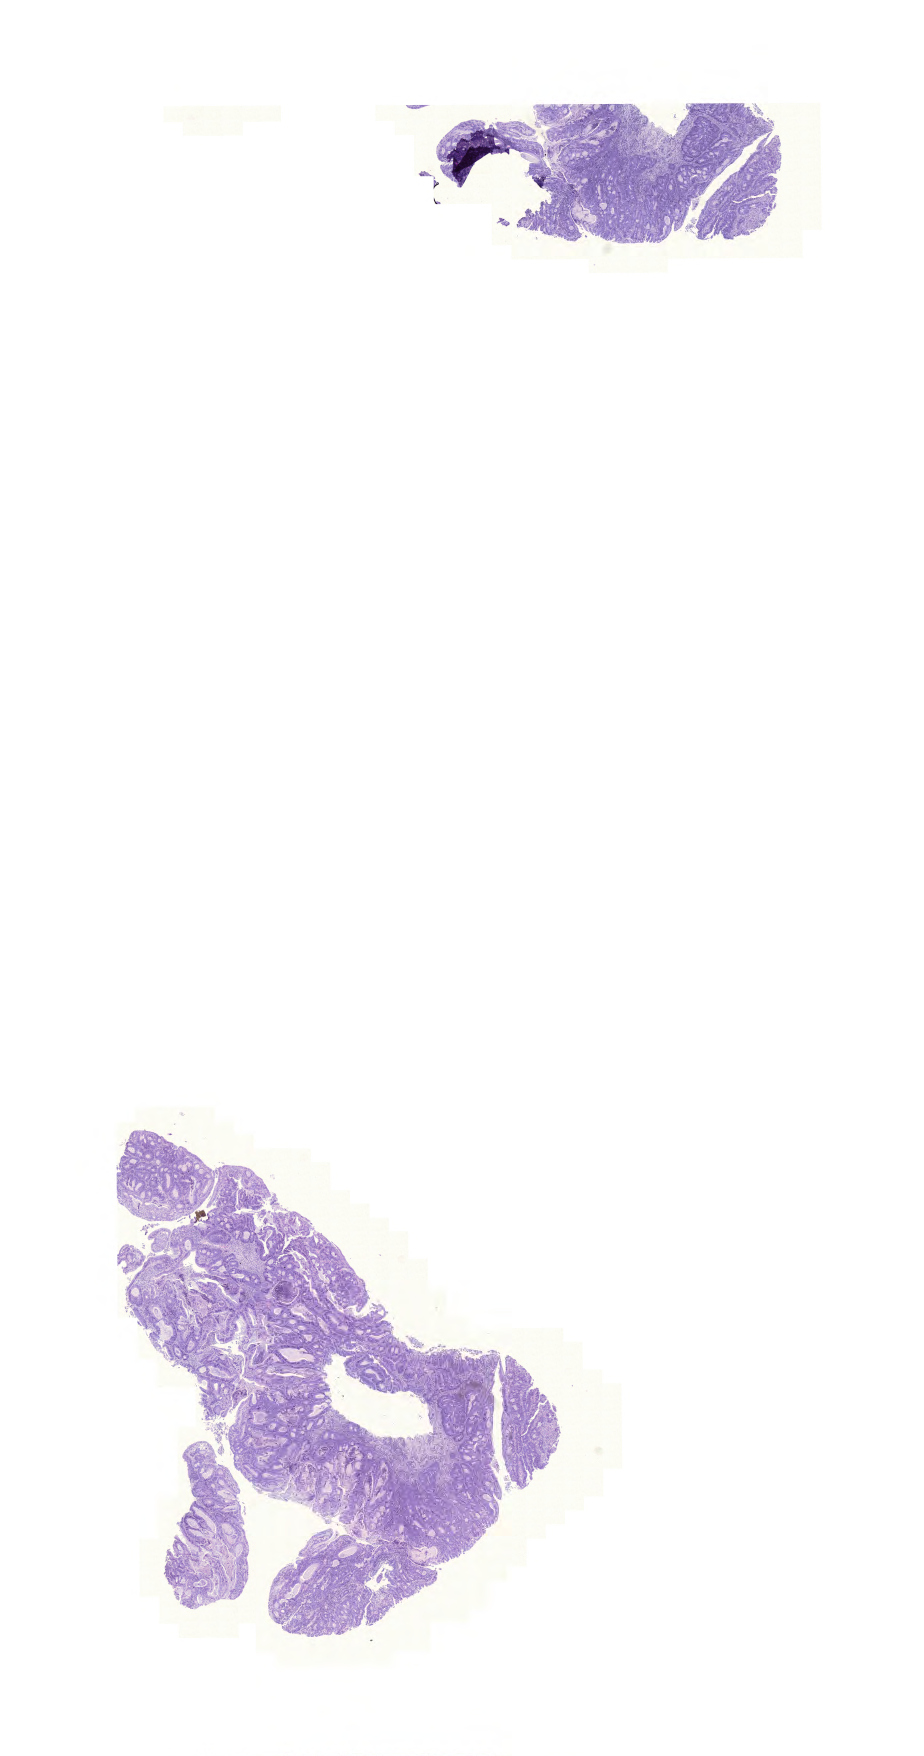
Whole-slide histology image, H&E — a low-resolution overview of the entire scanned area, about 13.7 x 26.1 mm (from a 20x scan). Formalin-fixed paraffin-embedded (FFPE) diagnostic section. Sample: primary tumour, colon. Male, age 74 years at initial diagnosis.
Pathologic diagnosis: Adenocarcinoma, NOS (transverse colon).